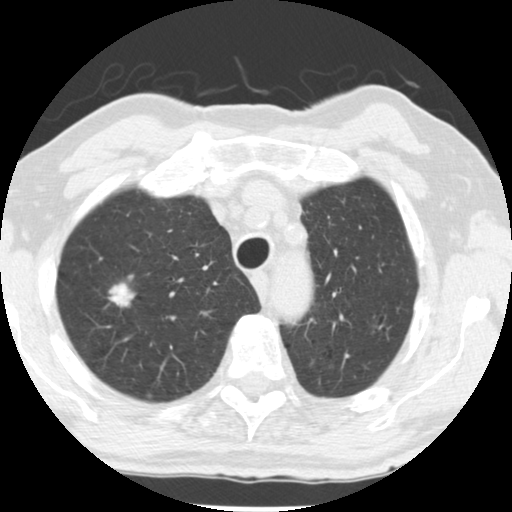
Low-dose screening chest CT, axial slice; baseline annual screen; lung window (W 1500 / L -600 HU); 2.5 mm slice thickness; slice 203 of 252 in the series; 512 × 512 image matrix, field of view 313 × 313 mm. Male, age 69 years at enrolment. Former smoker at enrolment.
- Expert-annotated lung lesion, bounding box (x1, y1, x2, y2) in pixels: (91, 270, 151, 327).
- The screening reader recorded 2 non-calcified nodules or masses ≥4 mm on this exam (right upper lobe, left upper lobe); which of them this box marks is not recorded.
- Official screen result: positive, change unspecified: nodule(s) >= 4 mm or enlarging nodule(s), mass(es), or other non-specific abnormalities suspicious for lung cancer.
- Participant outcome: lung cancer diagnosed 105 days after this screen — adenocarcinoma, NOS, right upper lobe, well differentiated (G1), stage IA (AJCC 6th edition), 17 mm at pathology.